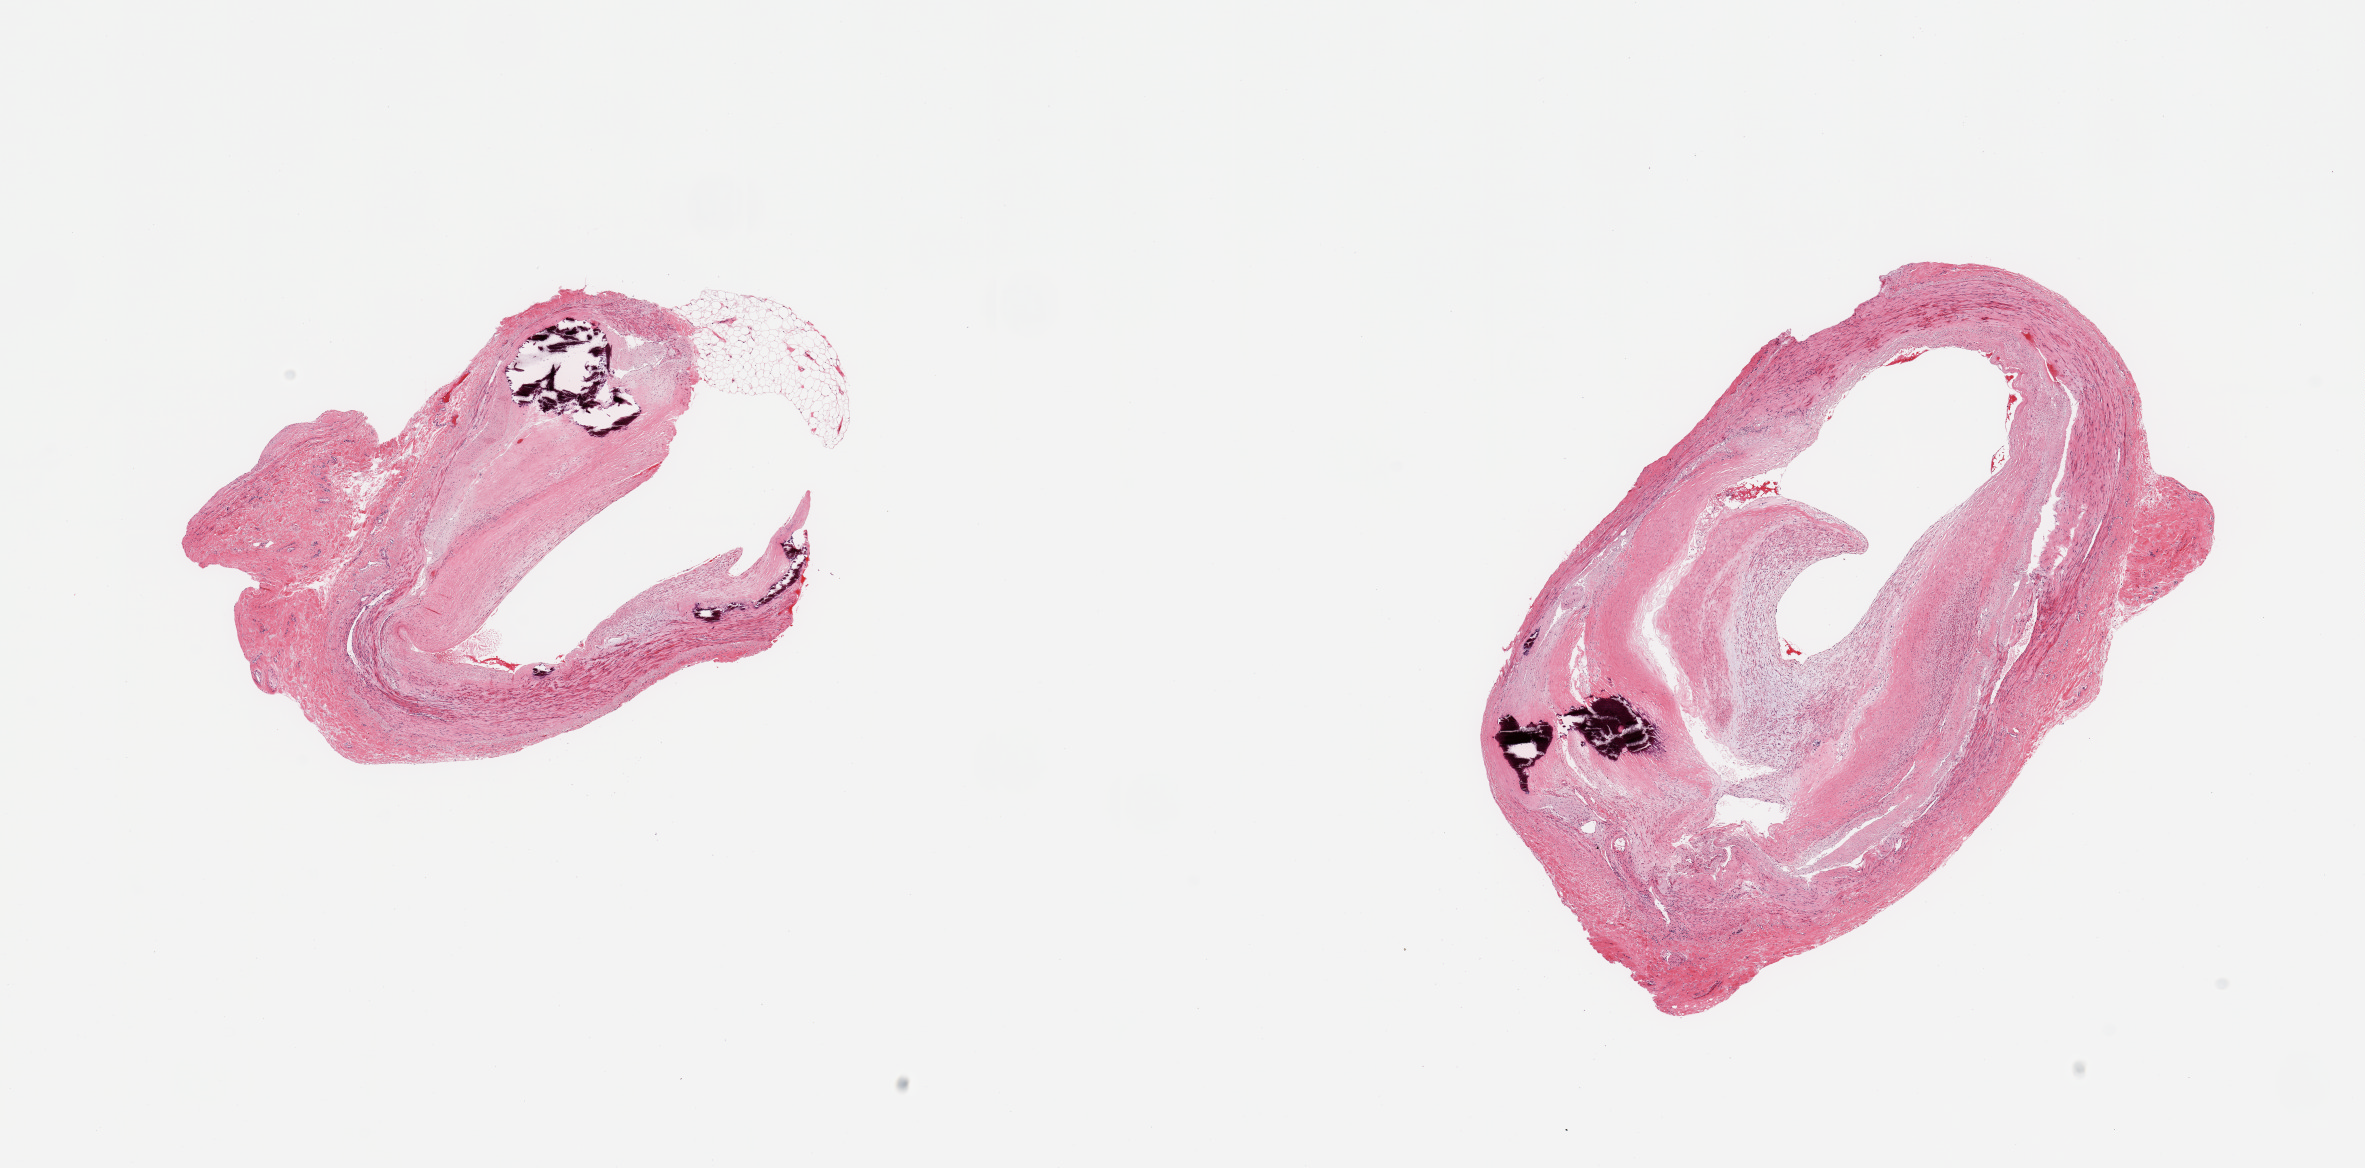
Haematoxylin and eosin whole-slide image, whole scanned area (about 18.7 x 9.2 mm, acquisition: 20x scan) shown as a low-resolution overview. PAXgene-fixed, paraffin-embedded tissue. Sampled site (target tissue): tibial artery. Donor tissue sample. Male donor.
* reviewer comment on this tissue sample: 2 pieces; uneven plane of sections; medial calcifications; fibrosclerotic plaque with luminal compromise